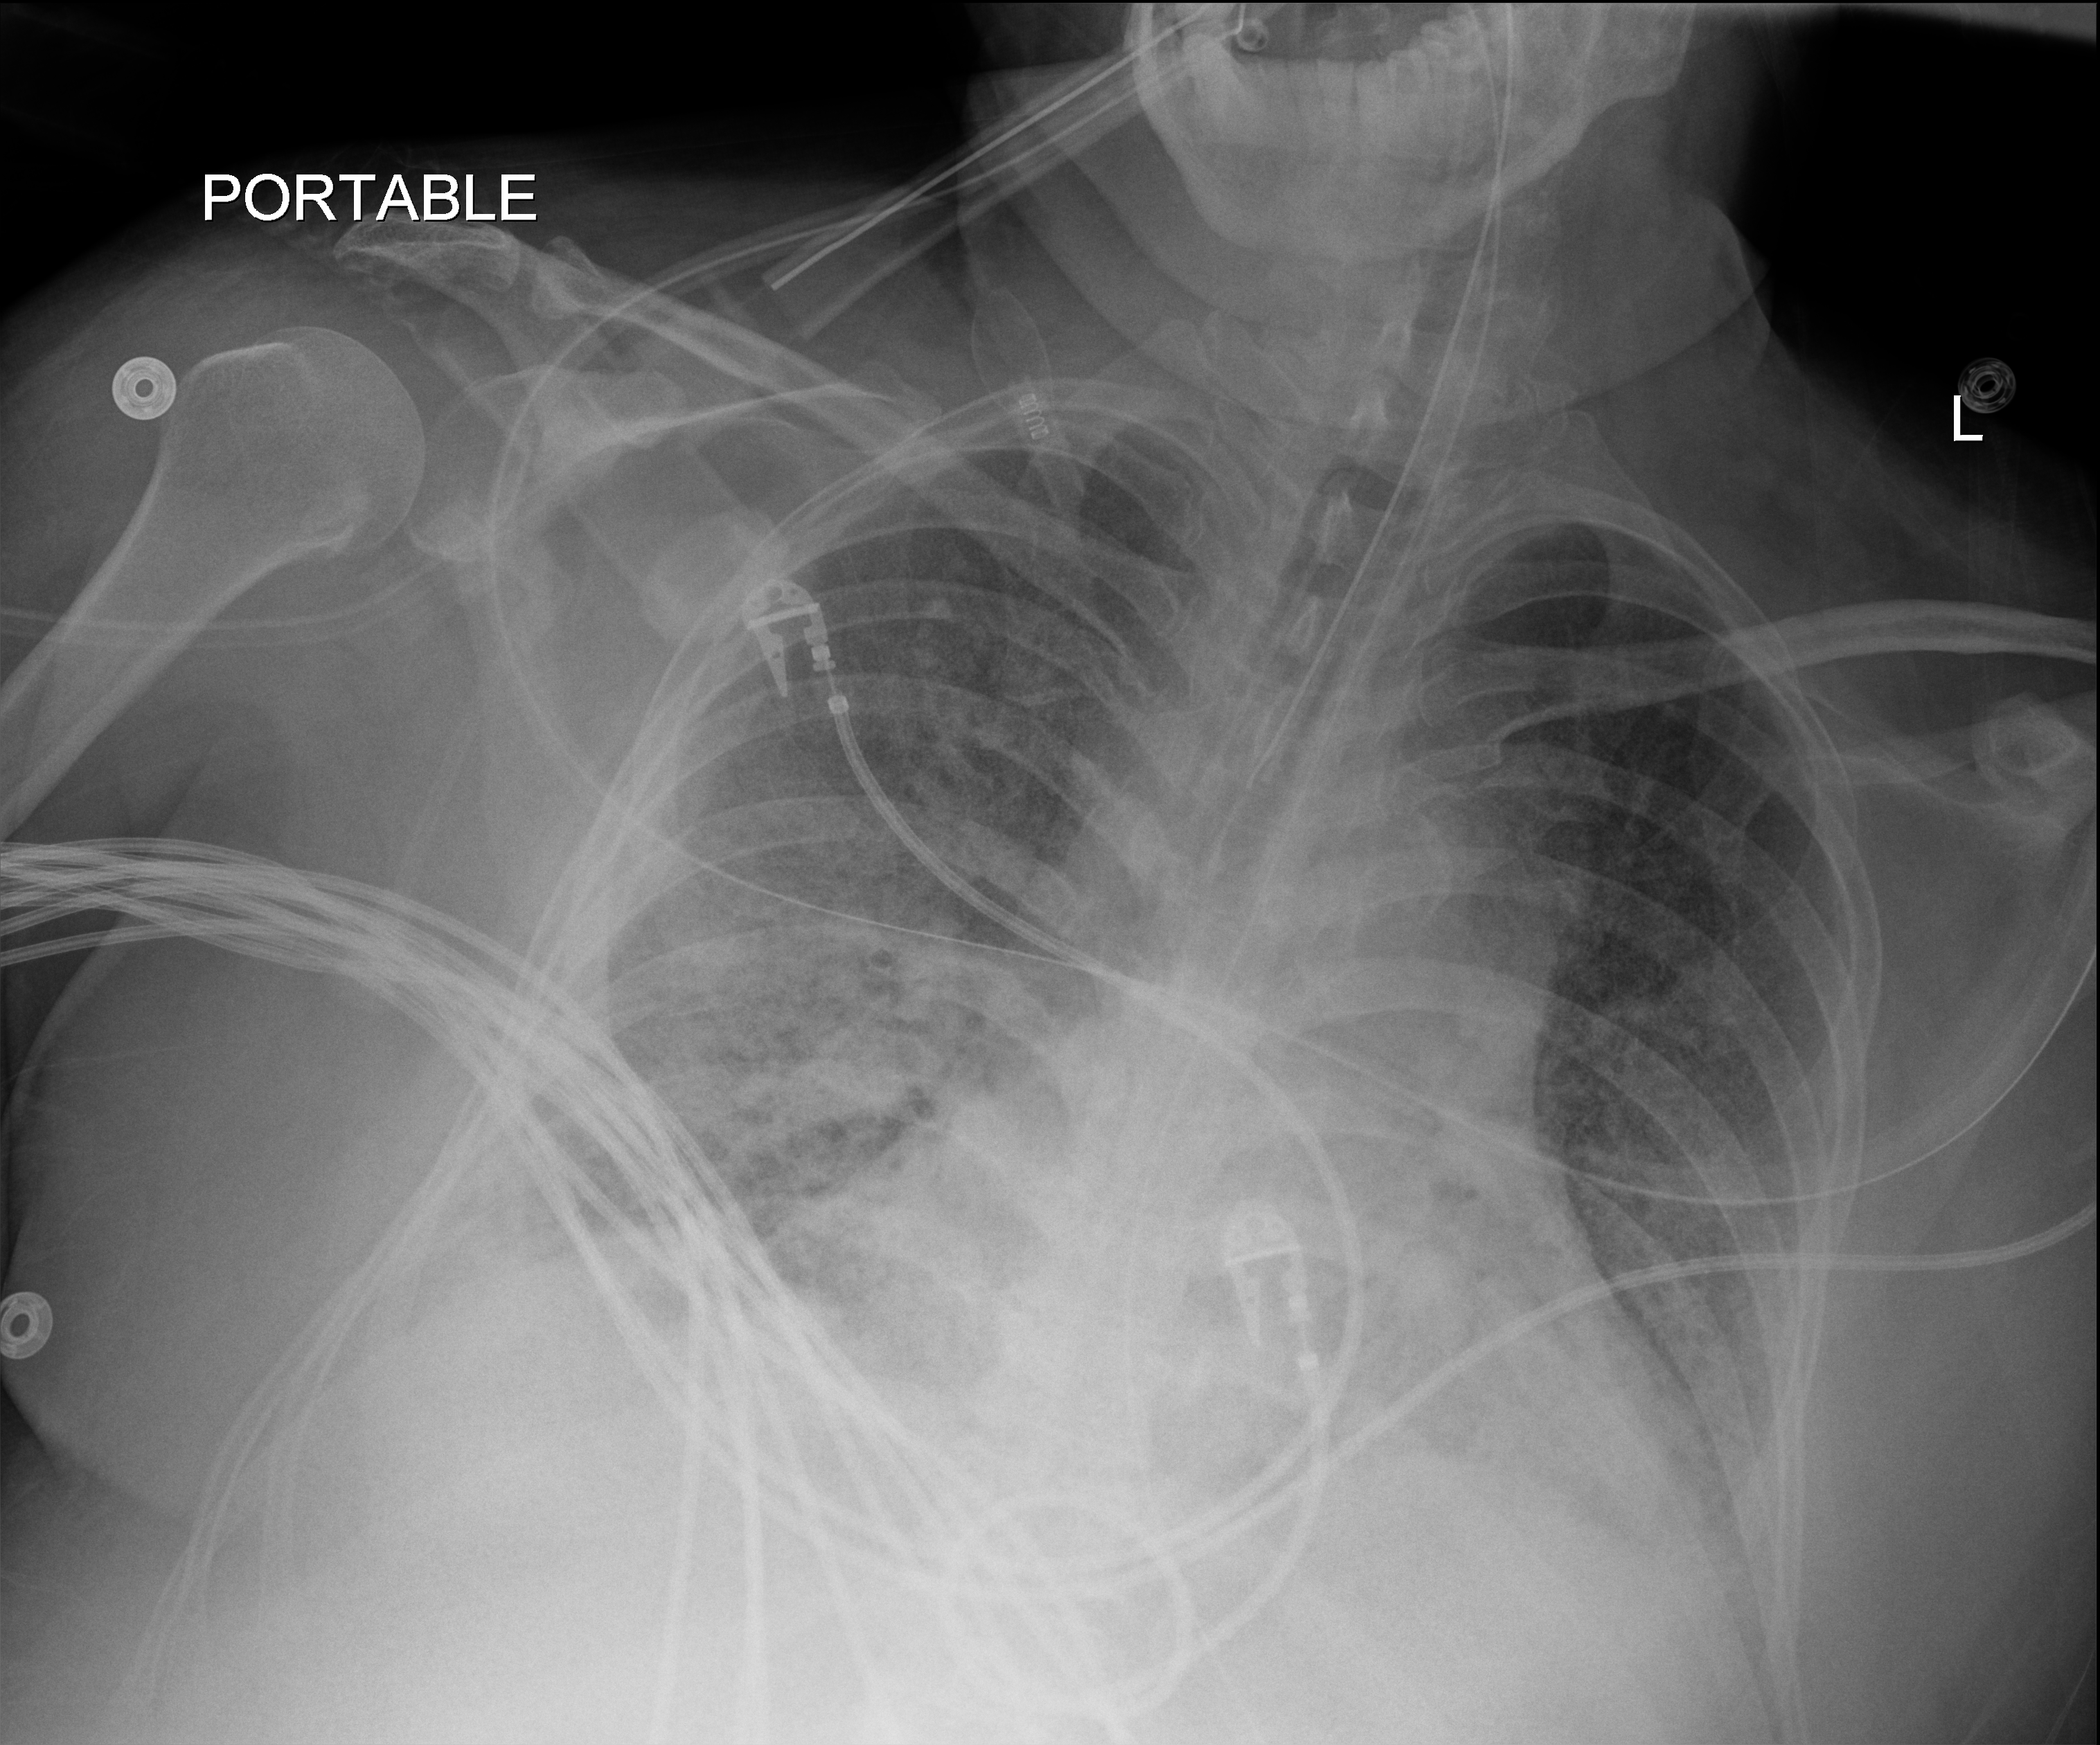
Bedside chest radiograph (digital radiography); anteroposterior (AP) projection. Adult patient hospitalised with COVID-19, age 18–59 years.
Admission-level facts for this patient (not findings on this image; timing relative to this image not recorded): other chronic lung disease (admission record): no; admitted to intensive care during this hospital stay: yes.